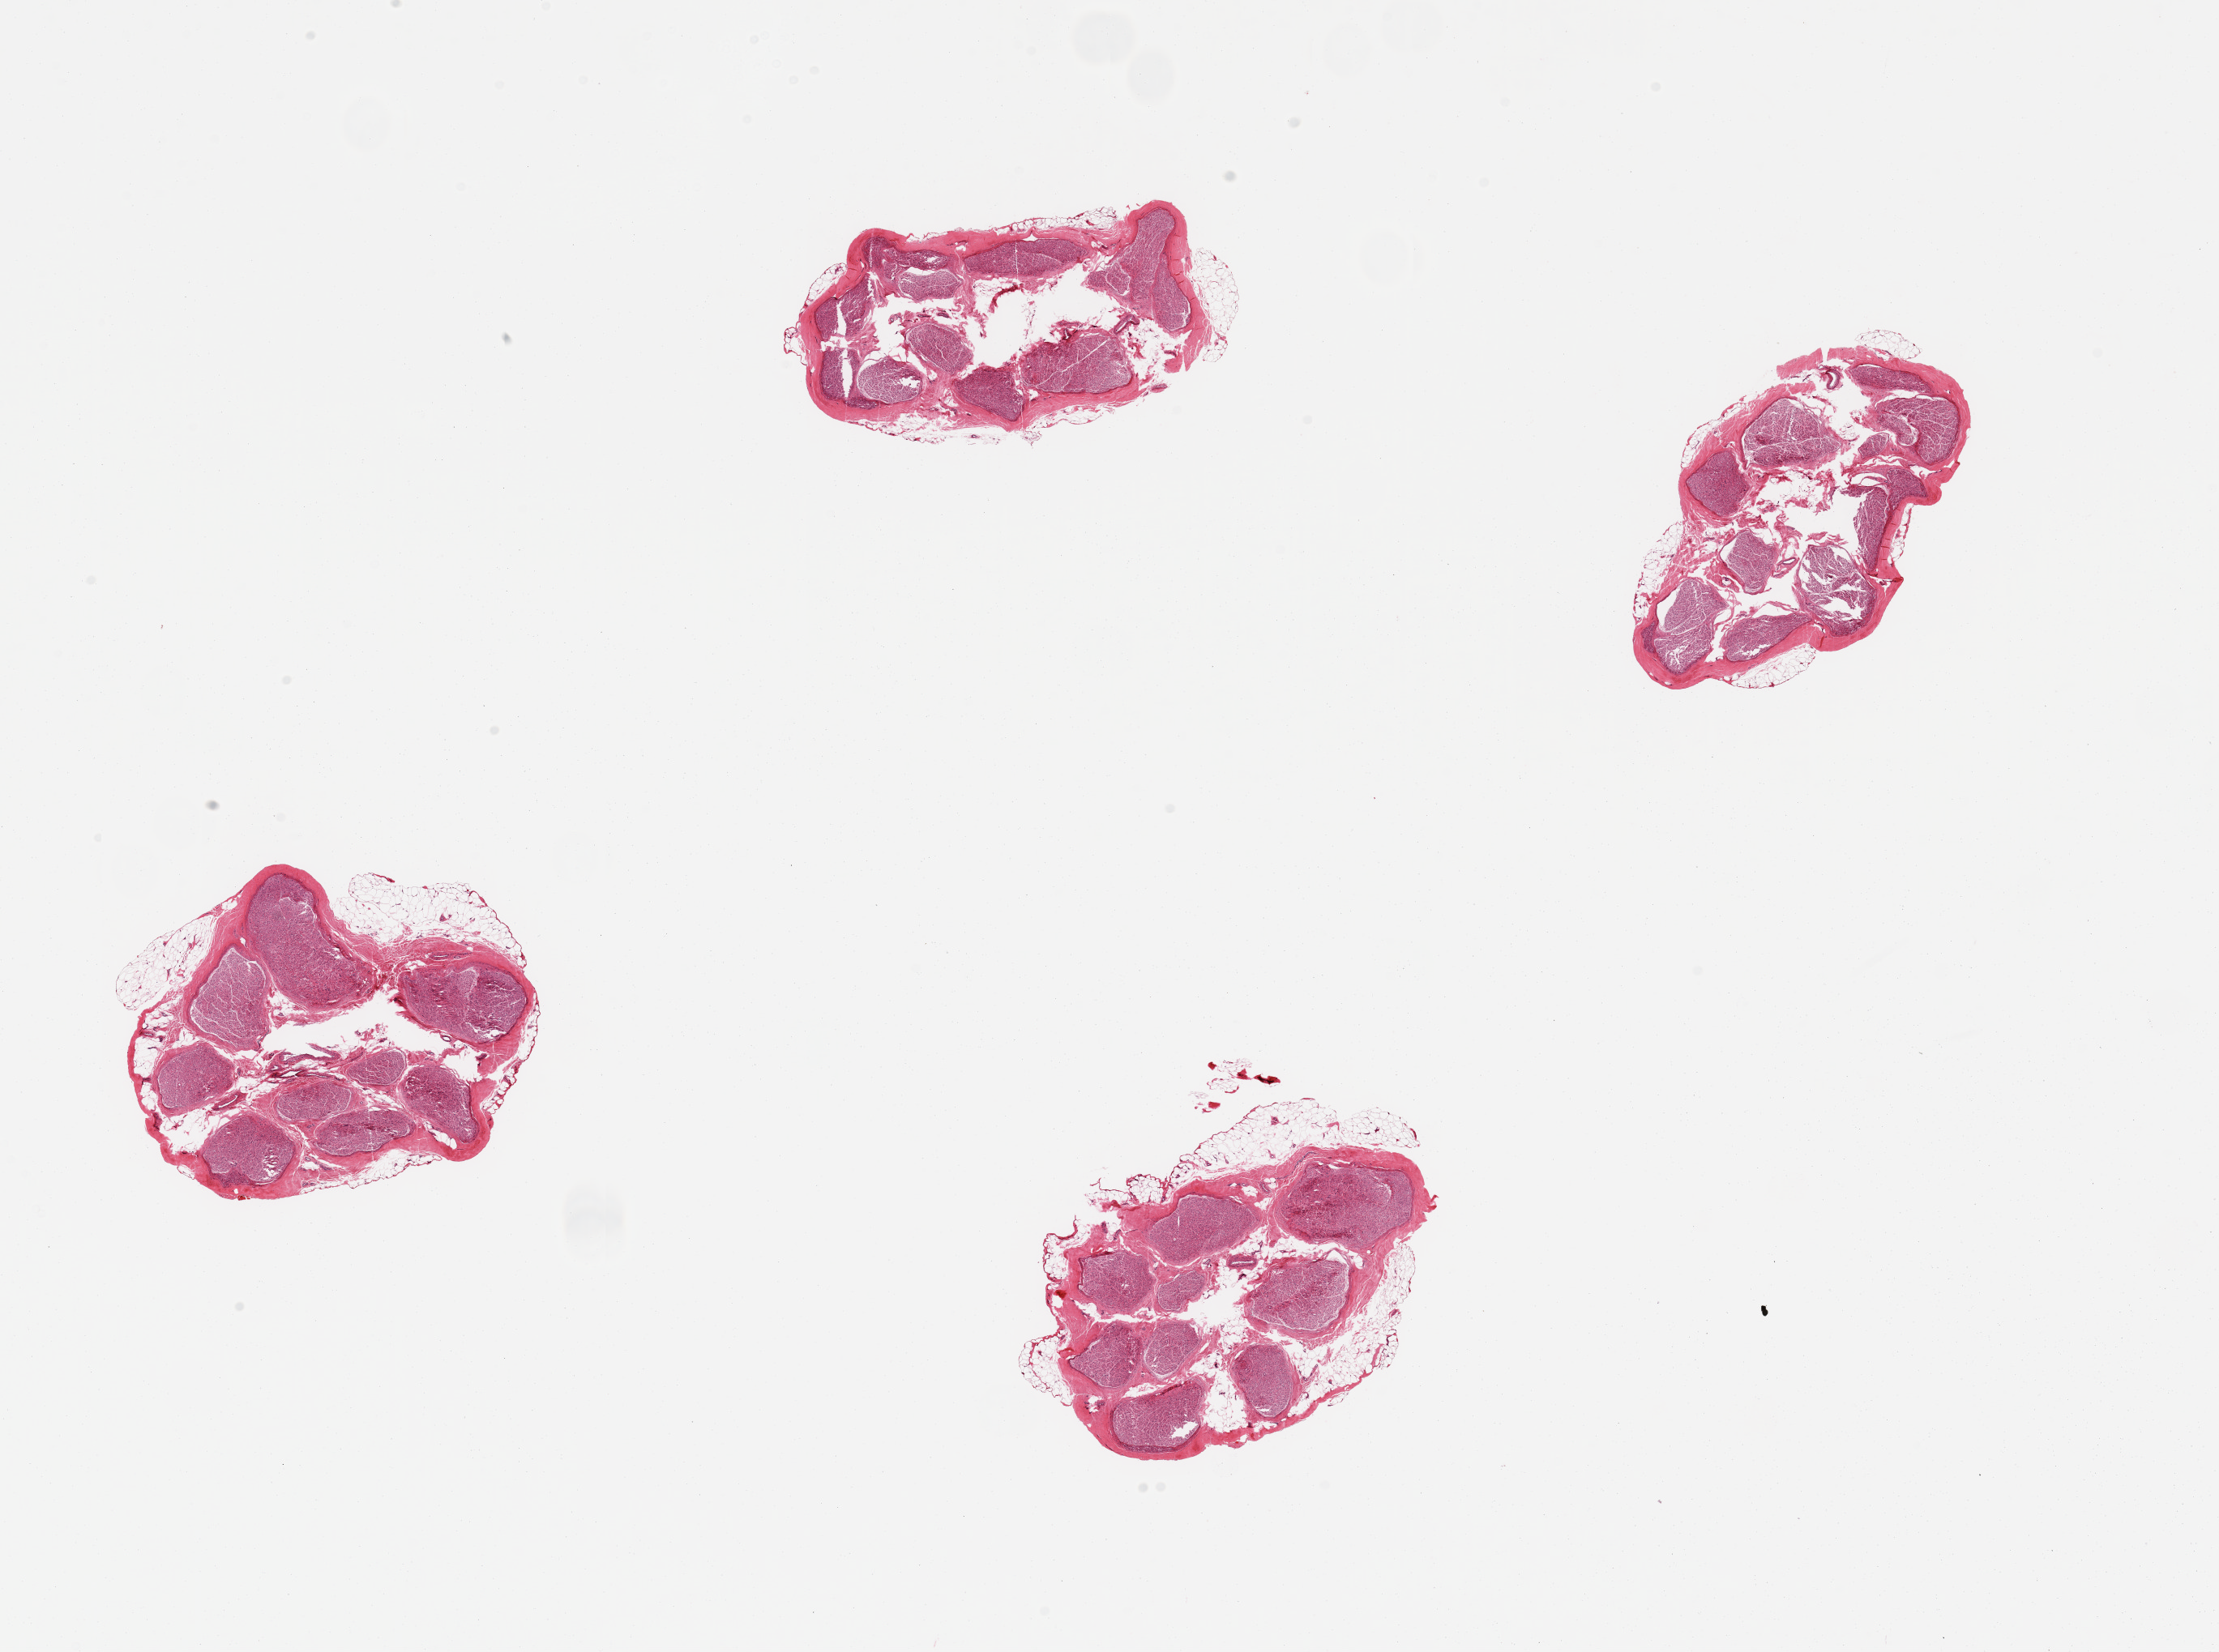
Hematoxylin and eosin (H&E) whole-slide image — low-resolution overview of the scanned area, about 21.7 x 16.1 mm (from a 20x scan), PAXgene-fixed paraffin-embedded (PFPE) section, sampled site (target tissue): tibial nerve, tissue donor sample. Donor sex: male.
Review note (as recorded): 4 pieces.